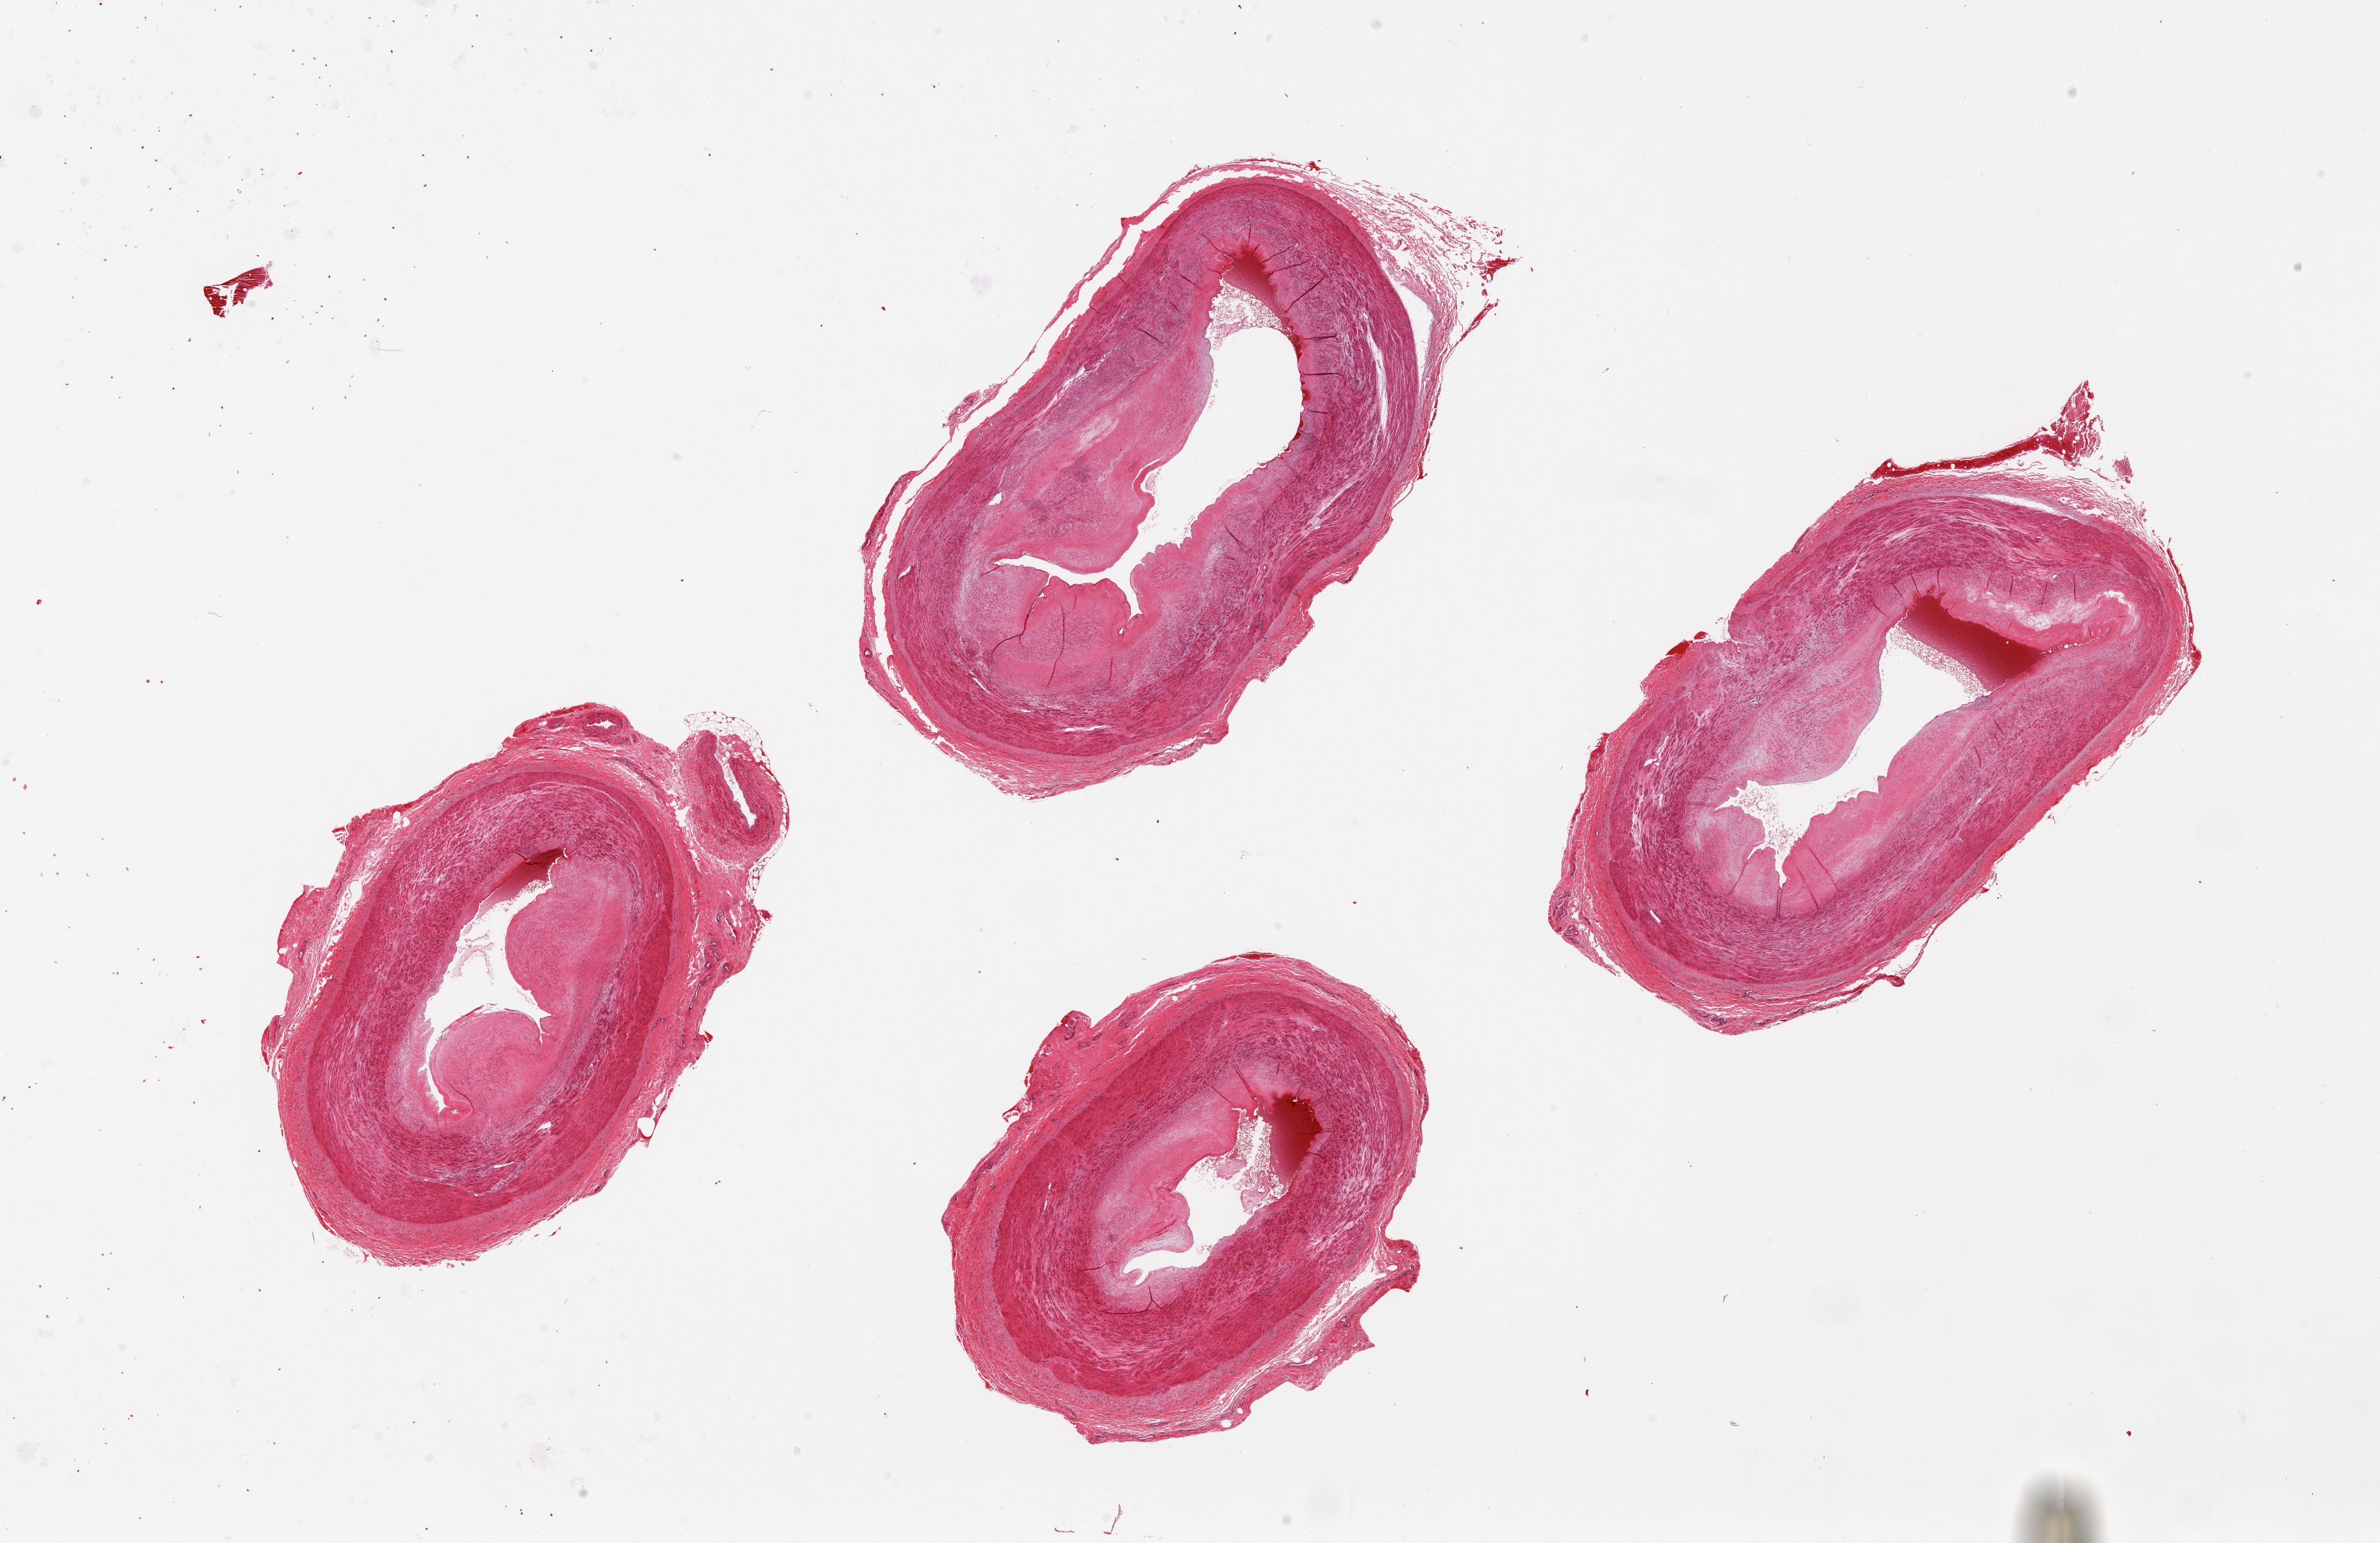
Digitized haematoxylin and eosin-stained section, whole scanned area (about 29.5 x 19.1 mm, slide scanned at 20x) shown as a low-resolution overview, PAXgene-fixed paraffin-embedded (PFPE) section, section of tibial artery (target tissue), donor tissue sample. Donor sex: male.
Review note (as recorded): 4 pieces, from 5.5x6.5 to 9x5mm; moderate intimal thickening.